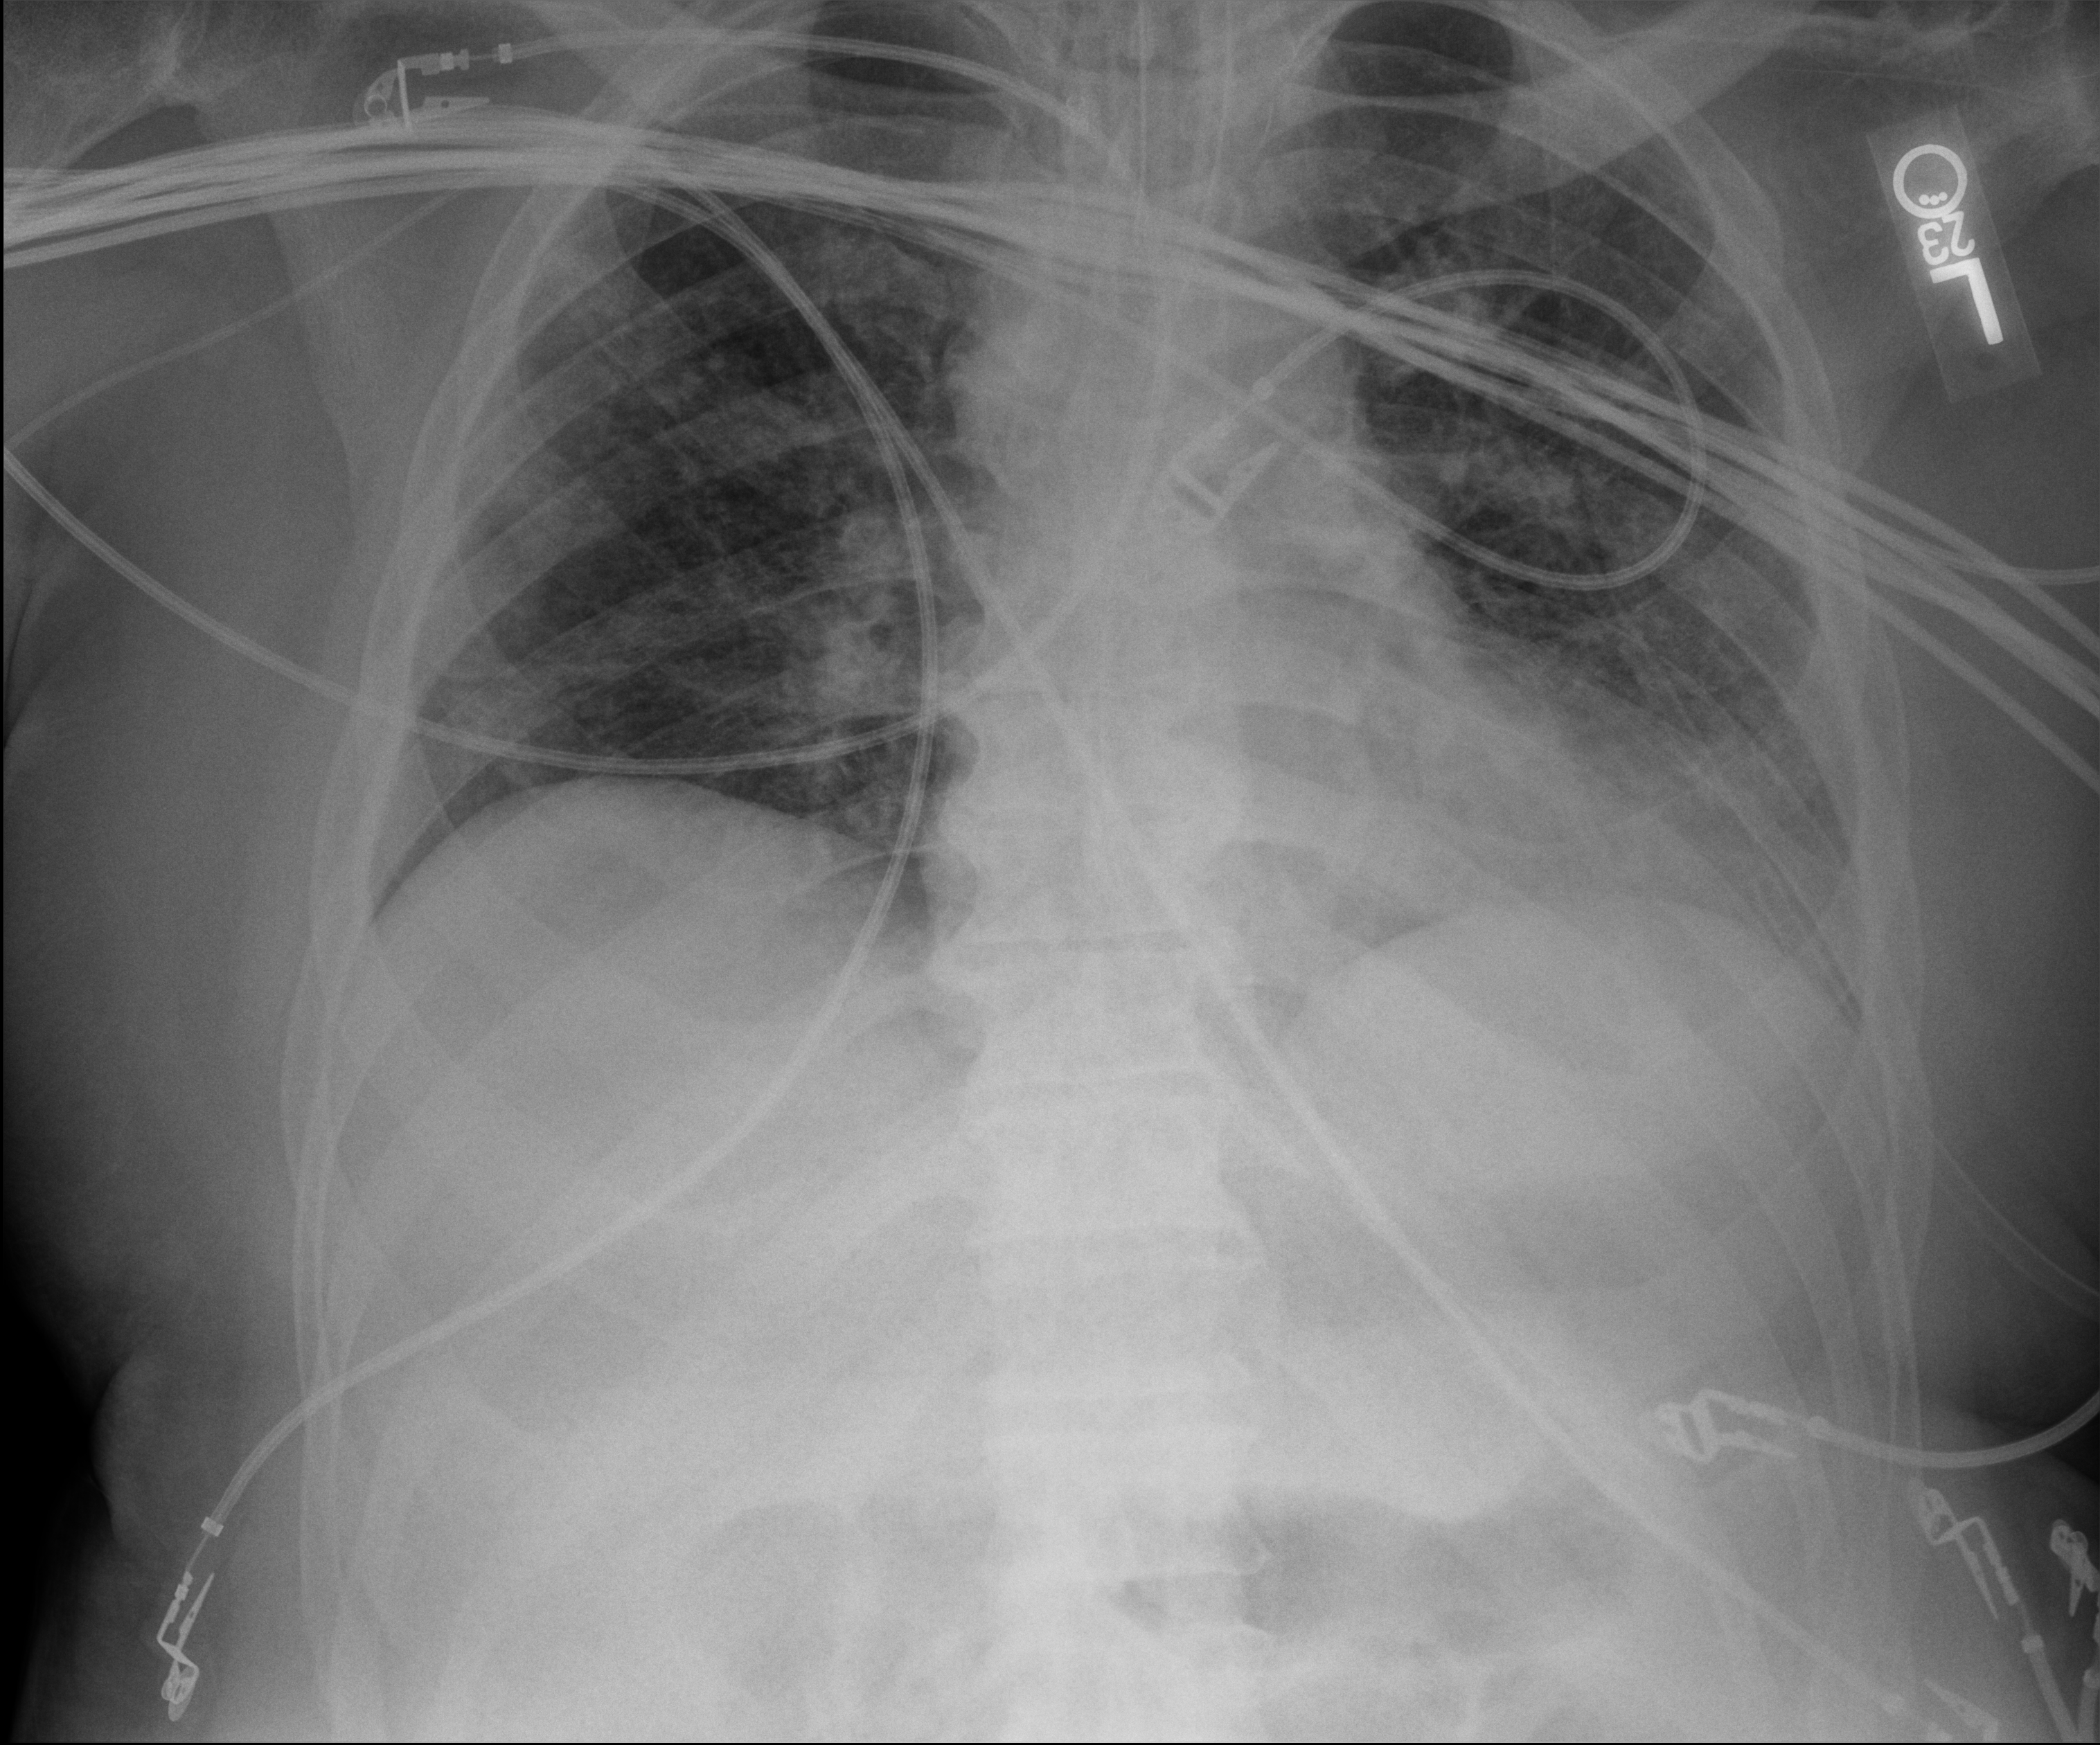
Portable chest radiograph, anteroposterior (AP) projection. Patient hospitalised with COVID-19; male, aged 18–59 years.
From the hospital-stay record, not from the radiograph (when in the stay this image was taken is not recorded): mechanically ventilated during this hospital stay: yes.